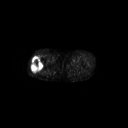
FDG PET of an extremity soft-tissue mass (from a PET/CT study), one axial slice. Position 244 of 267 along the scan axis. 3.27 mm slice thickness. 128 × 128 image matrix, field of view 700 × 700 mm. Male patient, age 43 years. Case-level facts recorded for this patient, not image findings: histological type: poorly differentiated synovial sarcoma; grade: high; site of the primary tumour: right buttock.
Outlined on this slice (expert contour drawn on MRI and transferred to this co-registered scan by the dataset authors):
- gross tumour volume including surrounding oedema: bounding box <30,58,43,73> (left, top, right, bottom; pixels)
- gross tumour volume (mass): <31,58,43,73>